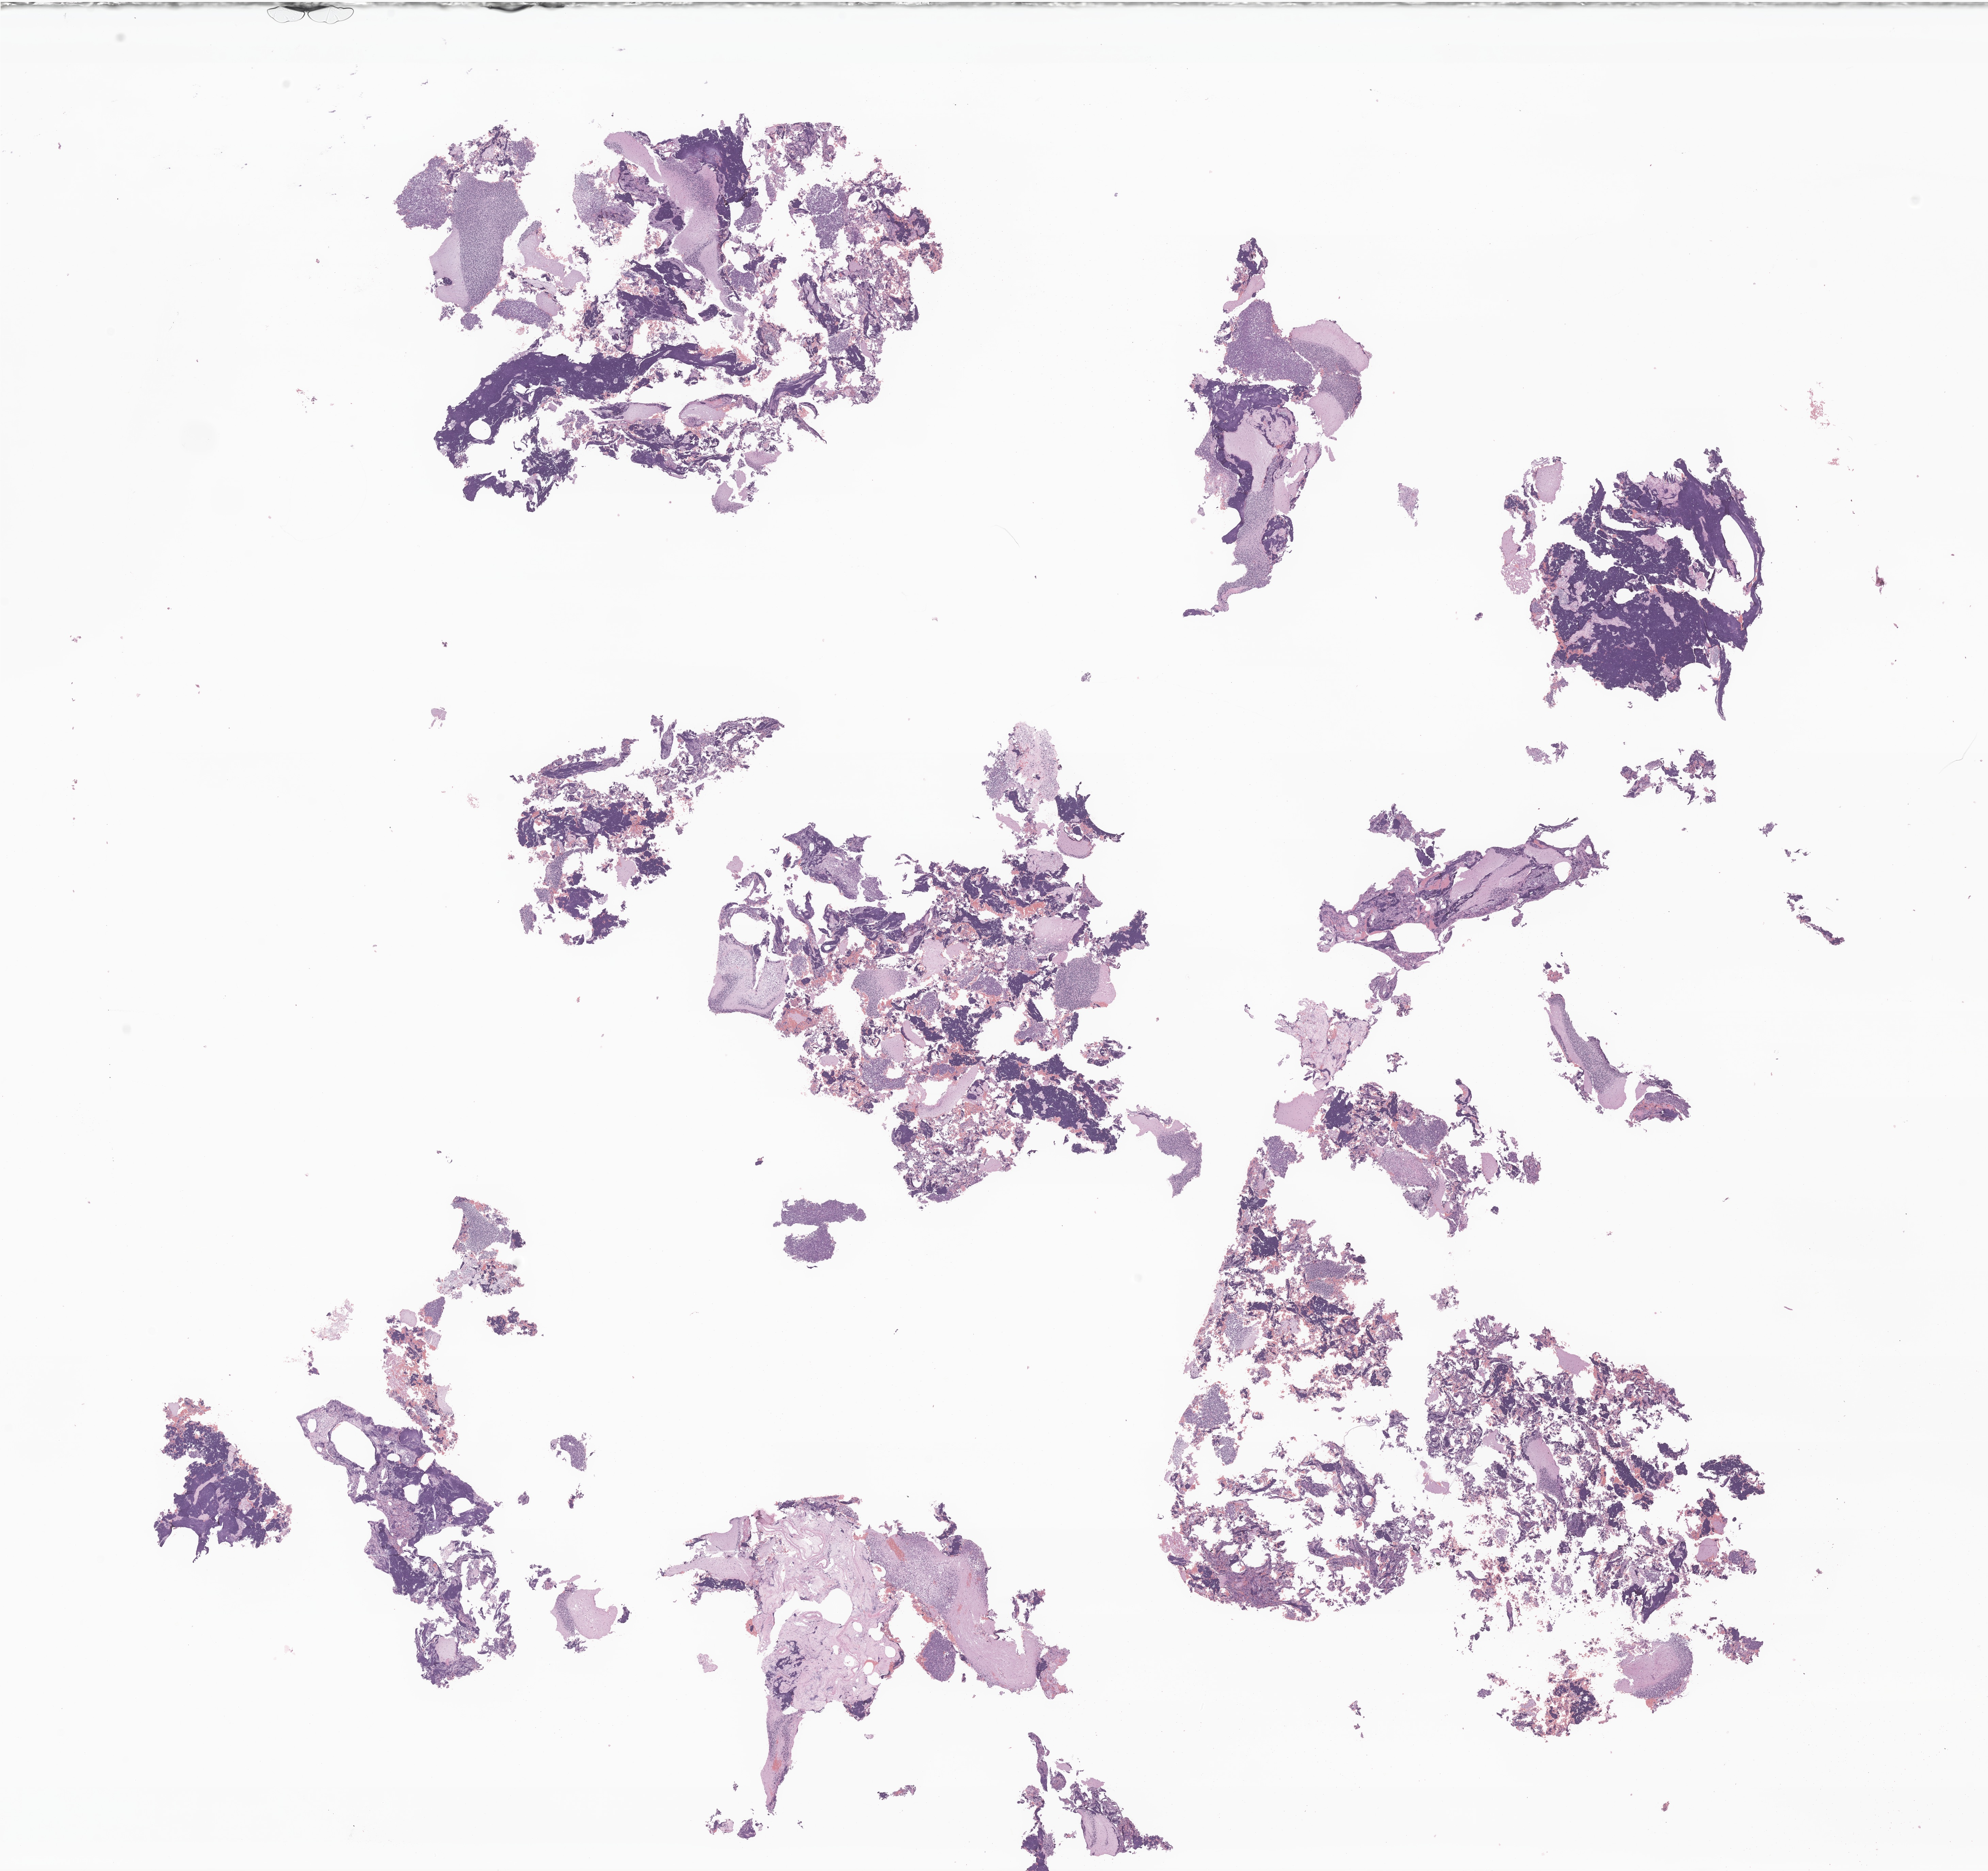
Whole-slide image, hematoxylin and eosin (H&E) stain of tumor tissue from the brain — low-resolution overview of the scanned area, about 24.6 x 23.2 mm. Formalin-fixed, paraffin-embedded (FFPE) tissue. Female patient, age 92 months.
* diagnosis (ICD-O-3 morphology term): Neoplasm, uncertain whether benign or malignant